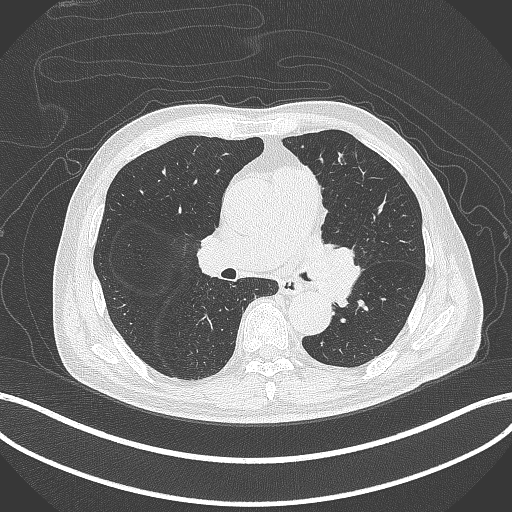
Chest CT, one axial slice. Reconstruction kernel B70f. Lung window (W 1500 / L -600 HU). 1 mm slice thickness. 512 × 512 image matrix, field of view 400 × 400 mm. Patient: male, 77 years. From the clinical record (not read from this slice): clinical TNM (as recorded): T3 N1 M0.
Structures marked on this image (rectangle marked by the reading radiologist):
- lung tumour (recorded histology: adenocarcinoma): box from (x=304, y=239) to (x=362, y=312) px